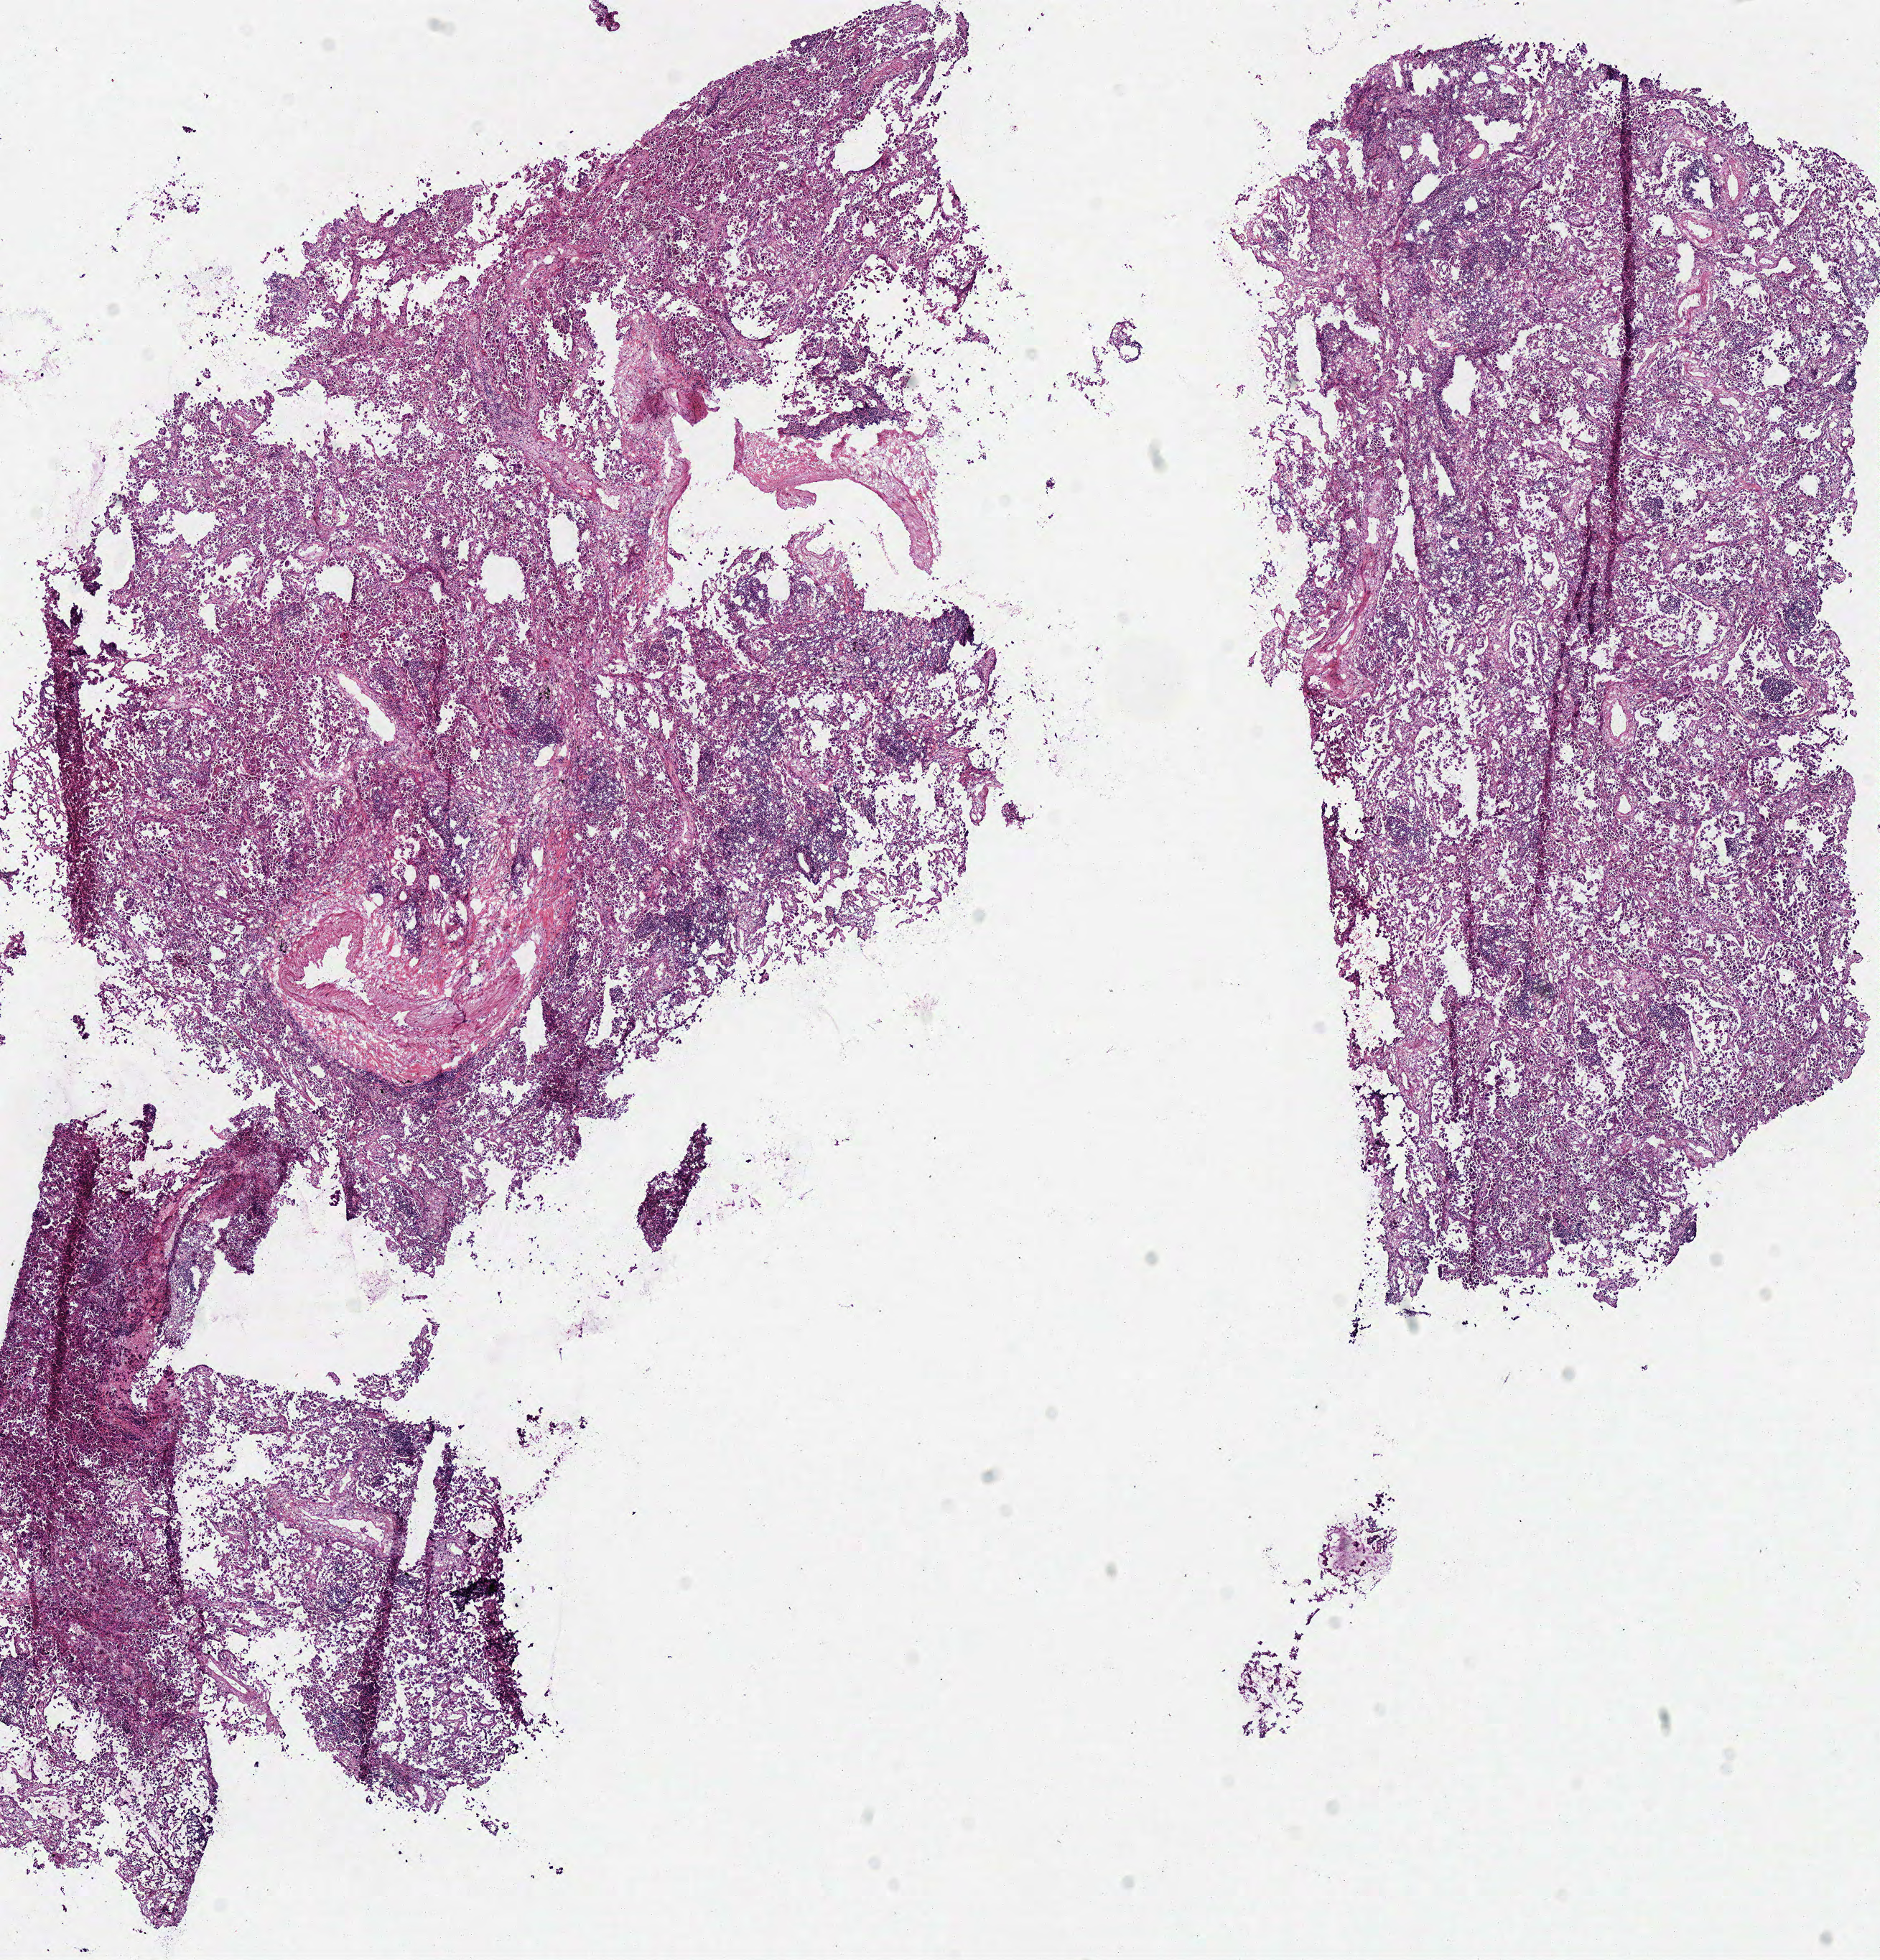
Digitized H&E tissue section (whole slide) — whole scanned area (about 10.3 x 10.8 mm) shown as a low-resolution overview. Frozen section from the bottom of the tissue portion. Sample: primary tumour, lung. Female, age 79 years at initial diagnosis. Pathologist review of this section (percent, as recorded): tumour cells 85%, tumour nuclei 70%, normal cells 0%, stromal cells 15%, necrosis 0%.
AJCC pathologic stage: IB (6th edition). Diagnosis: Adenocarcinoma, NOS (lower lobe, lung). TNM: T2 N0 M0. Laterality: right.